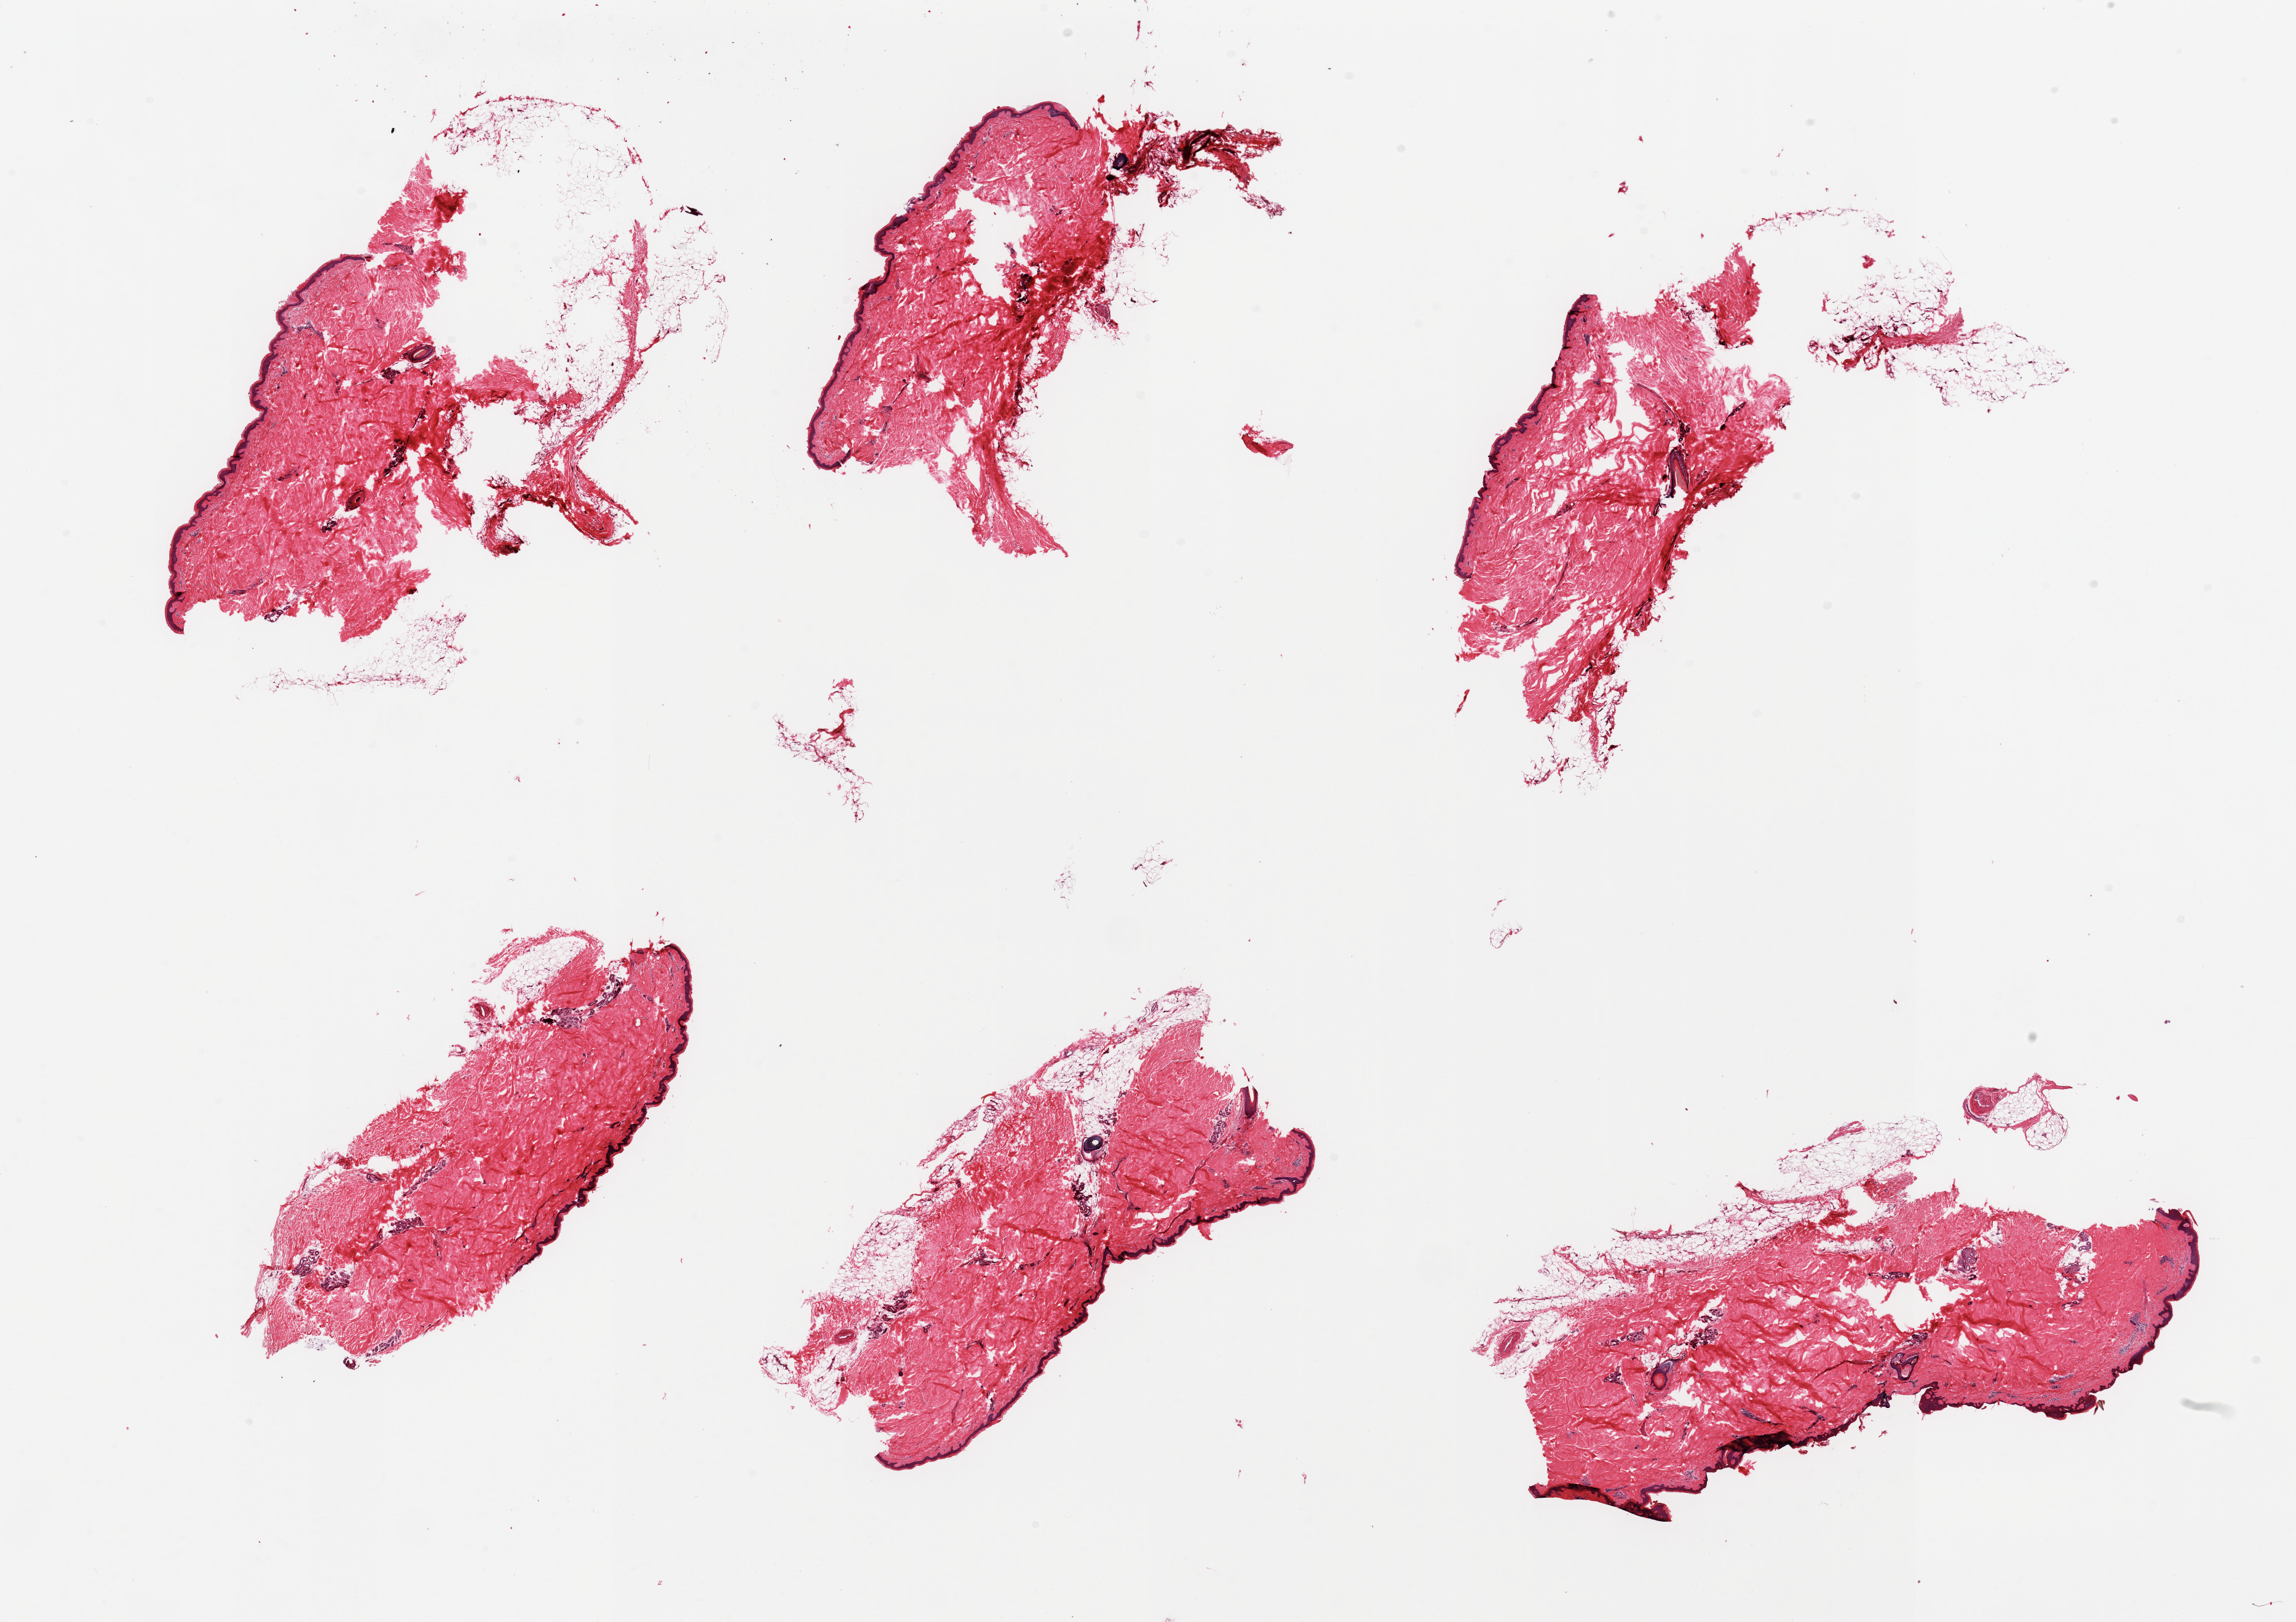
Whole-slide image, haematoxylin and eosin stain — a low-resolution overview of the entire scanned area, about 29.5 x 20.9 mm (slide scanned at 20x), PAXgene-fixed, paraffin-embedded tissue, section of skin of lower leg (target tissue), donor tissue sample.
Reviewer comment on this tissue sample: 6 fragmented pieces; moderate untrimmed subcutaneous fat; 5% dermal fat.